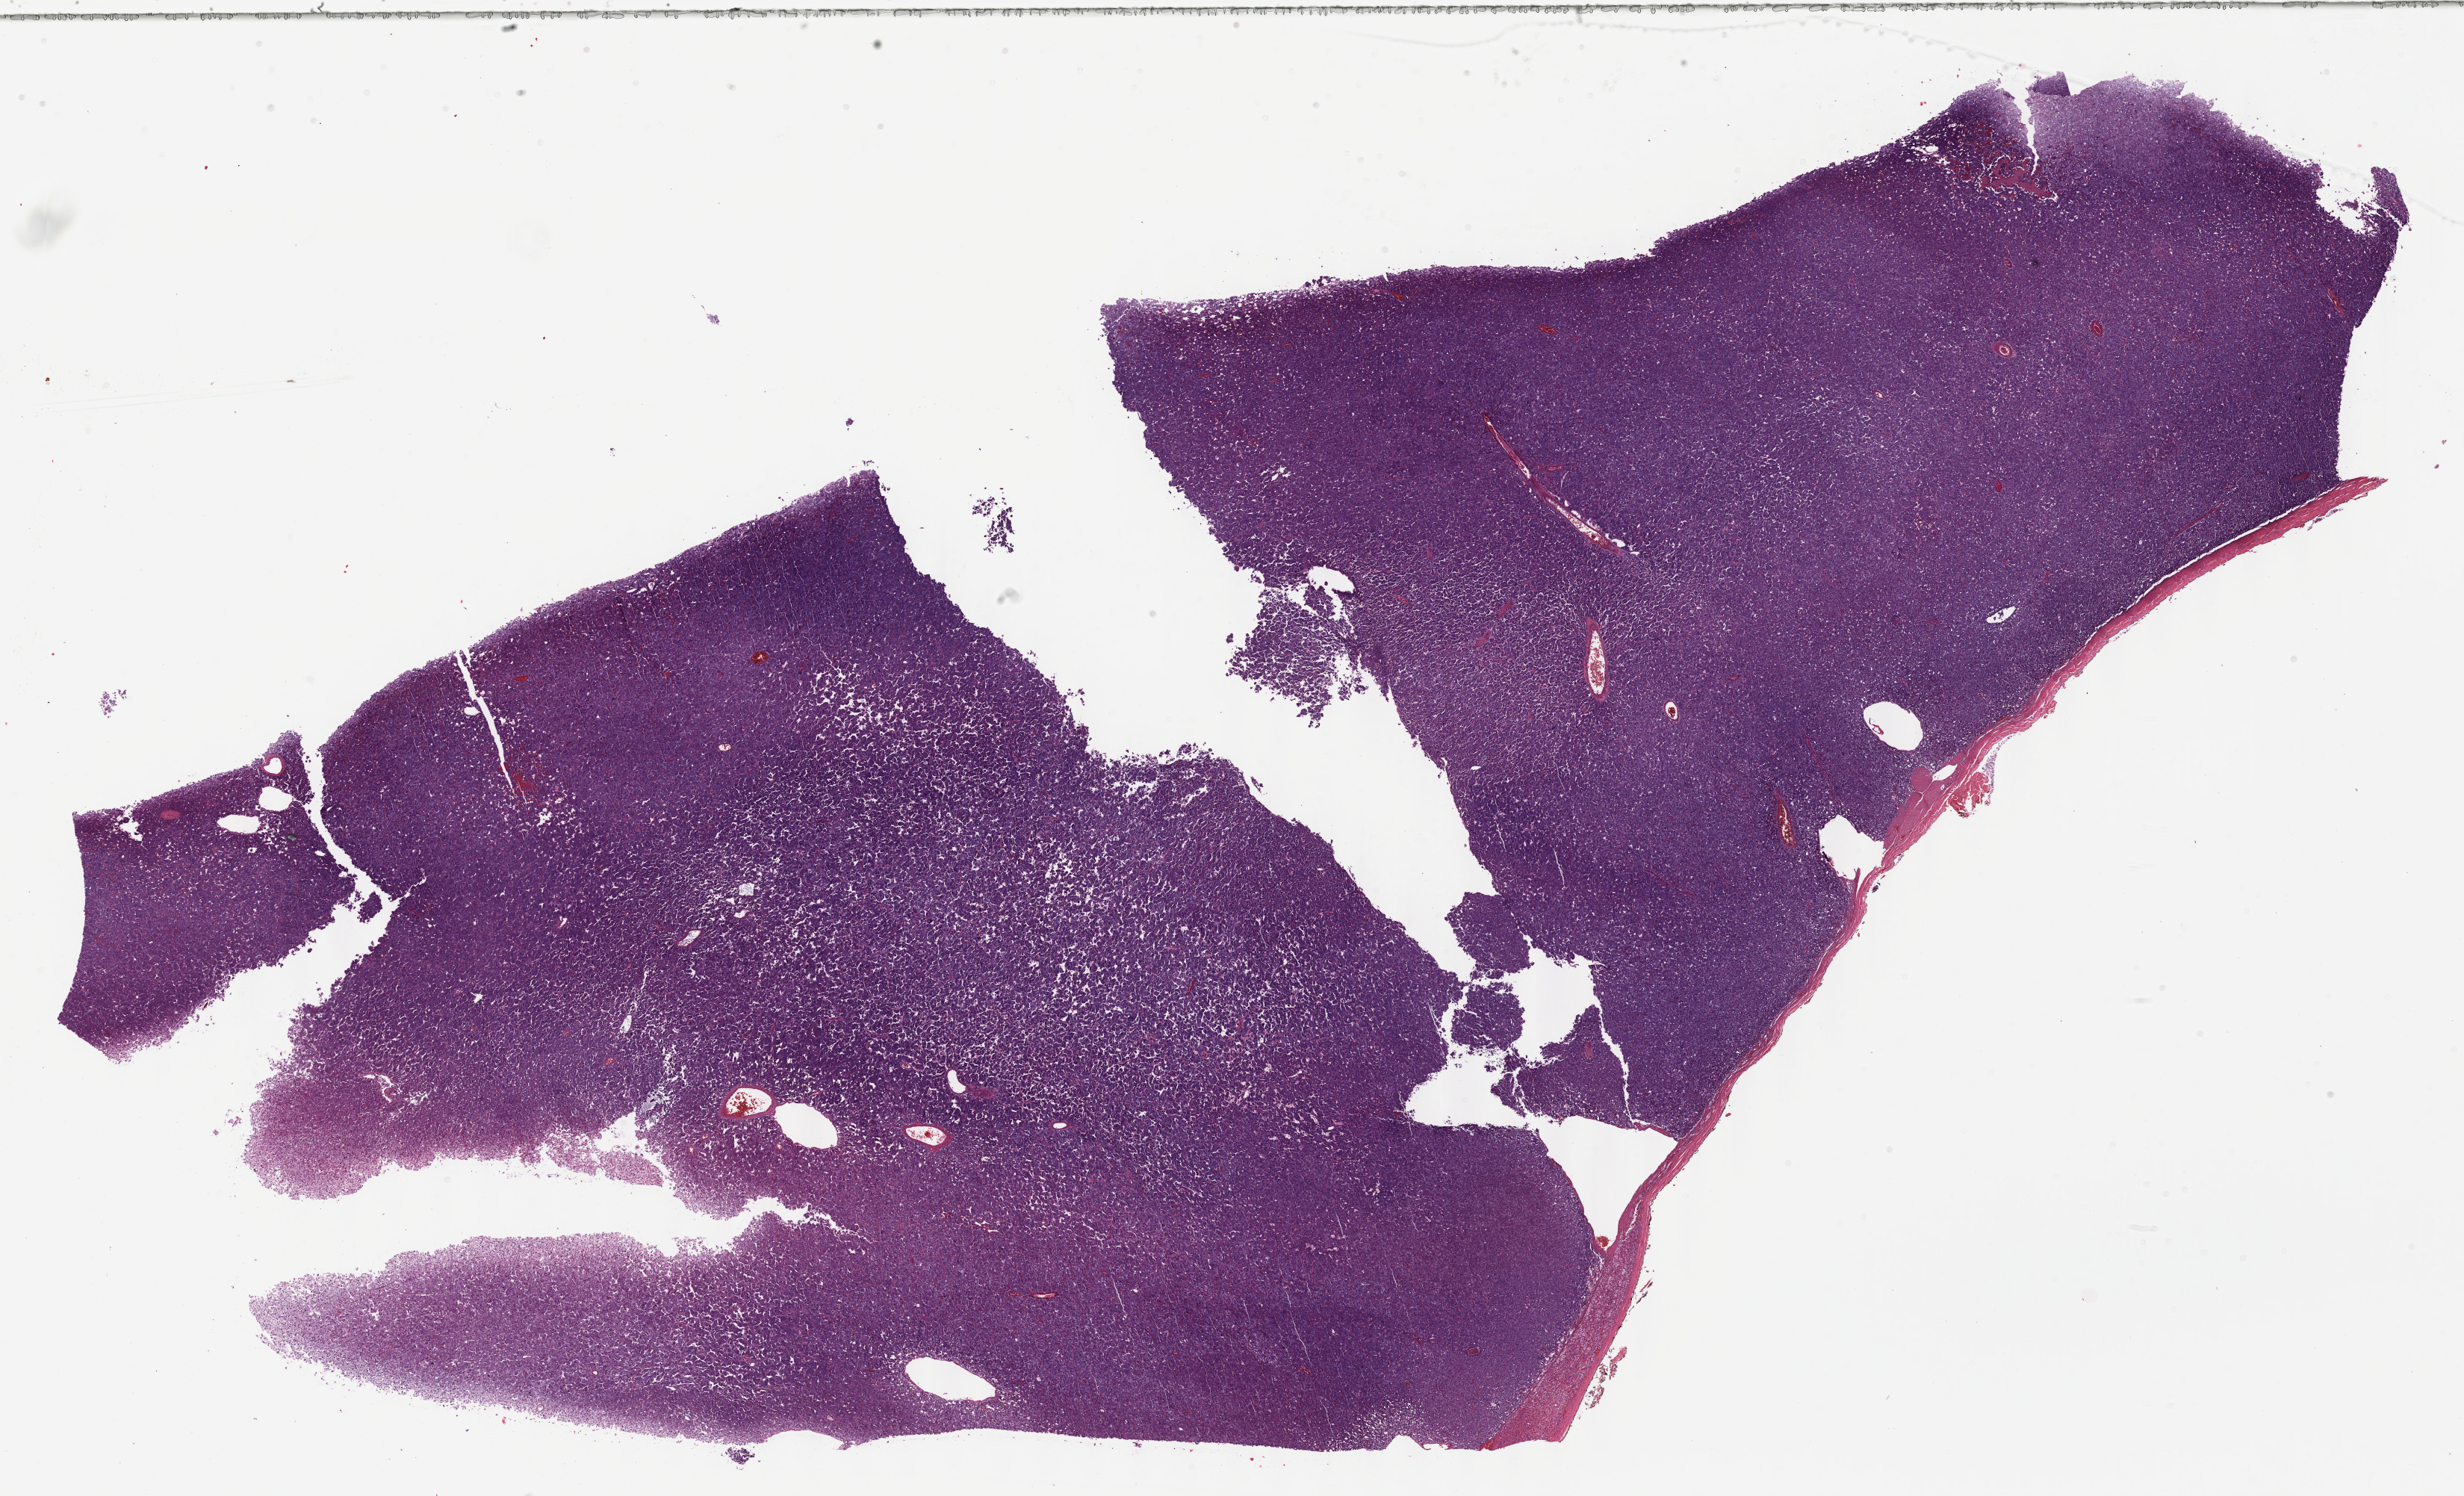
Whole-slide histology image, H&E, whole scanned area (about 26.7 x 16.2 mm, from a 40x scan) shown as a low-resolution overview. Formalin-fixed paraffin-embedded (FFPE) diagnostic section. Primary tumour sample from the adrenal gland. Female, age 37 years at initial diagnosis.
Pathologic diagnosis: Pheochromocytoma, malignant.